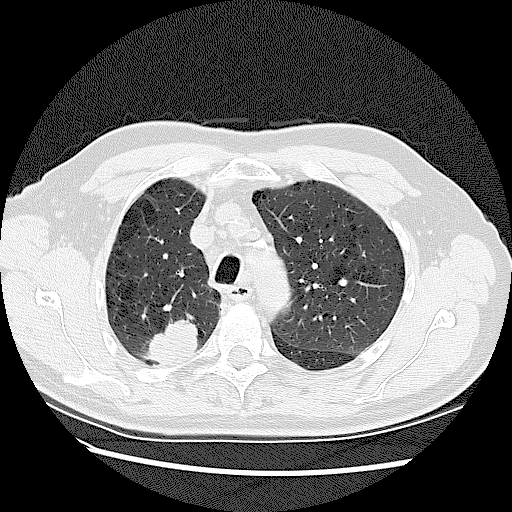
Chest CT (low-dose screening protocol), one axial image; first (baseline) screen; lung window (W 1500 / L -600 HU); 2.5 mm slice thickness; lung (sharp) reconstruction kernel (LUNG); 120 kVp; slice 33 of 128 in the series; 512 × 512 image matrix. Male, age 72 years at enrolment. Current smoker at enrolment.
Expert reader's lesion annotation, bounding box (x1, y1, x2, y2) in pixels: (137, 309, 213, 375). The screening reader recorded 2 non-calcified nodules or masses ≥4 mm on this exam; which of them this box marks is not recorded.